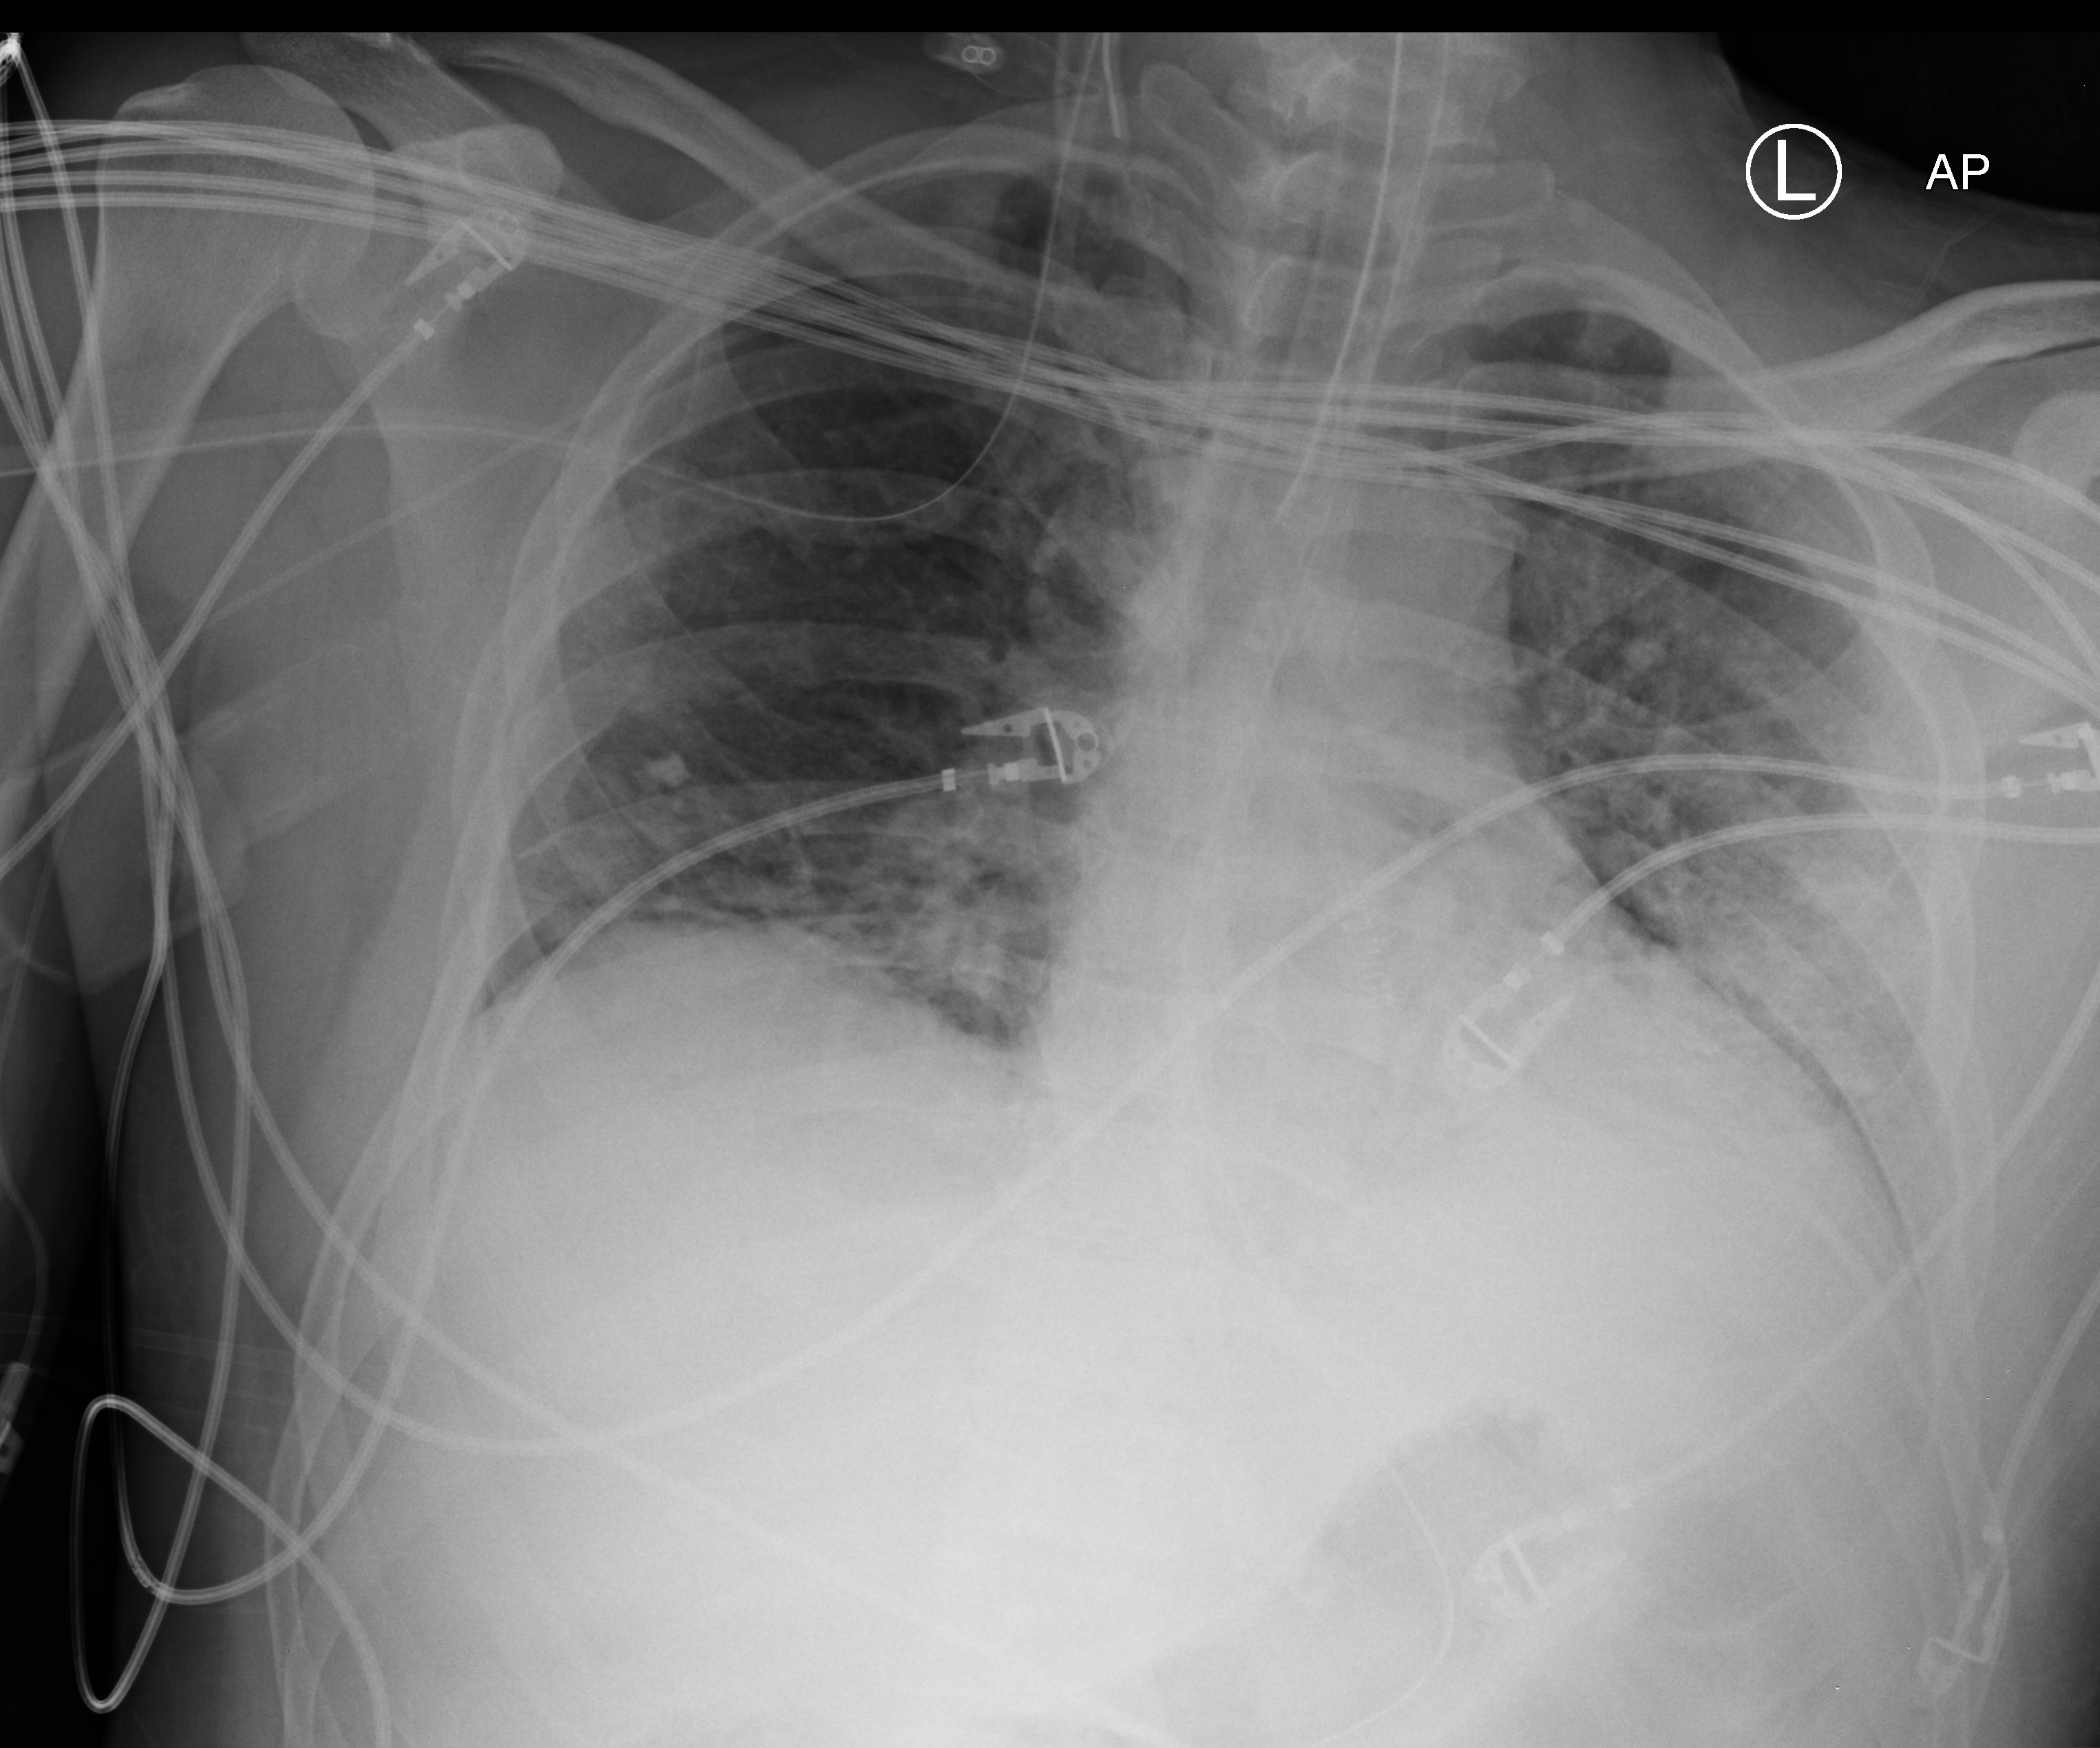
Bedside chest radiograph (computed radiography), anteroposterior (AP) projection. Male patient hospitalised with COVID-19, age 18–59 years.
Admission-level facts for this patient (not findings on this image; timing relative to this image not recorded): other chronic lung disease (admission record): no; admitted to intensive care during this hospital stay: no.